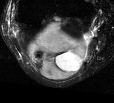
MRI of an extremity soft-tissue mass, one axial slice. T2-weighted fat-saturated. MR volume resampled by the dataset authors to the PET/CT grid (not the native acquisition matrix). 3.27 mm slice thickness. 114 × 103 image matrix, field of view 111 × 101 mm. Female patient. Case-level facts recorded for this patient, not image findings: histological type: liposarcoma; site of the primary tumour: right thigh.
Structures marked on this image (expert contour drawn on MRI and transferred to this co-registered scan by the dataset authors):
- gross tumour volume (mass): bounding box [x1, y1, x2, y2] px = [25, 20, 96, 81]